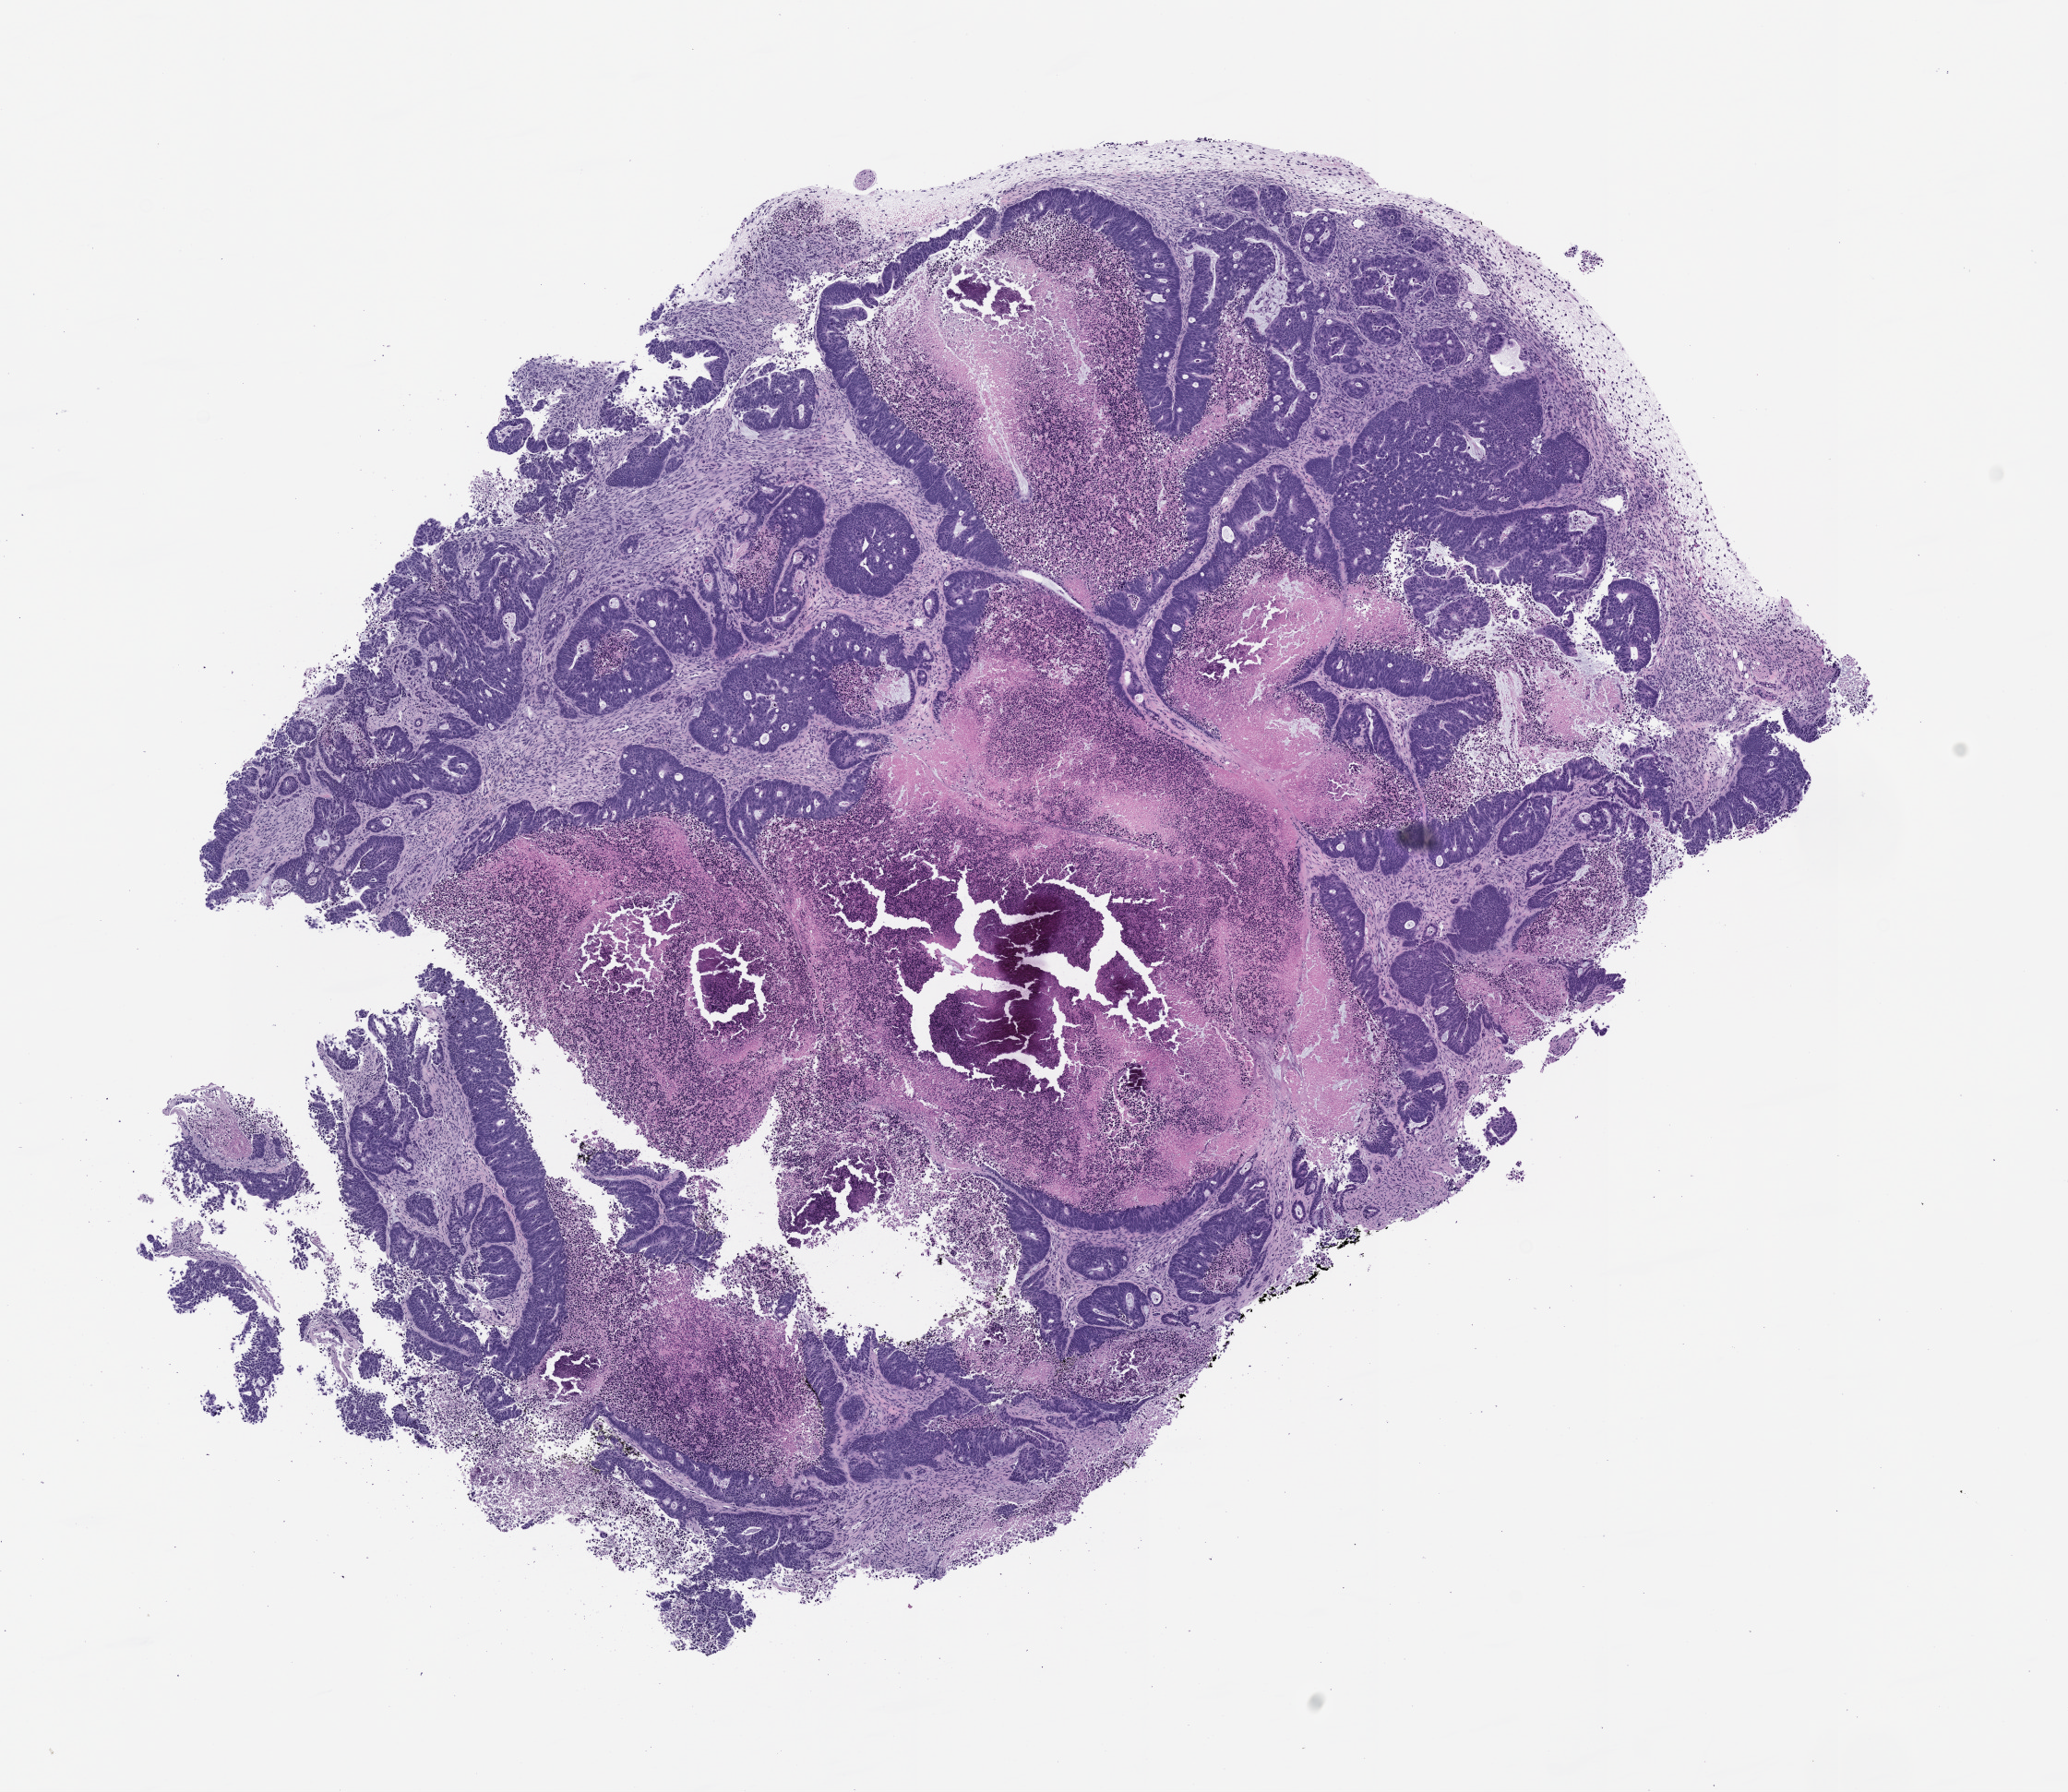
Whole-slide image, haematoxylin and eosin: patient-derived xenograft (human tumor grown in a mouse), passage 1 — low-resolution overview of the scanned area, about 9.0 x 7.8 mm. Formalin-fixed, paraffin-embedded (FFPE) tissue. Tumor site category: colon.
• originating patient diagnosis: Colon Adenocarcinoma